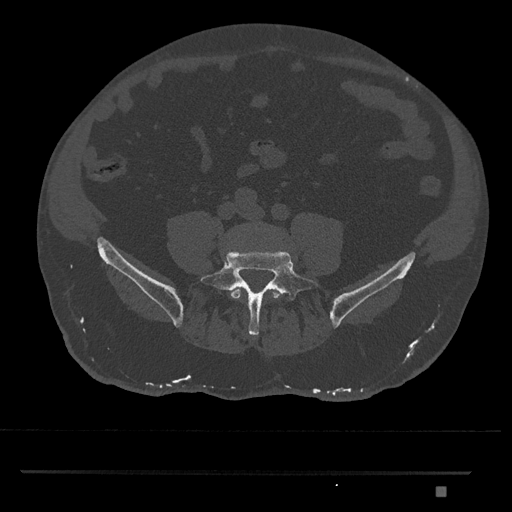
CT including the spine, one axial slice; position 569 of 1134 along the scan axis; 120 kVp; bone window (W 1800 / L 400 HU); 0.5 mm slice thickness; 512 × 512 image matrix, field of view 429 × 429 mm. Male patient, age 65 years. Case-level facts recorded for this patient, not image findings: primary cancer: prostate.
Annotated regions visible in this slice (semi-automatically segmented with operator editing):
- L4 vertebra: bounding box (x1, y1, x2, y2) in pixels: (230, 287, 282, 300)
- L5 vertebra: (200, 249, 321, 338)